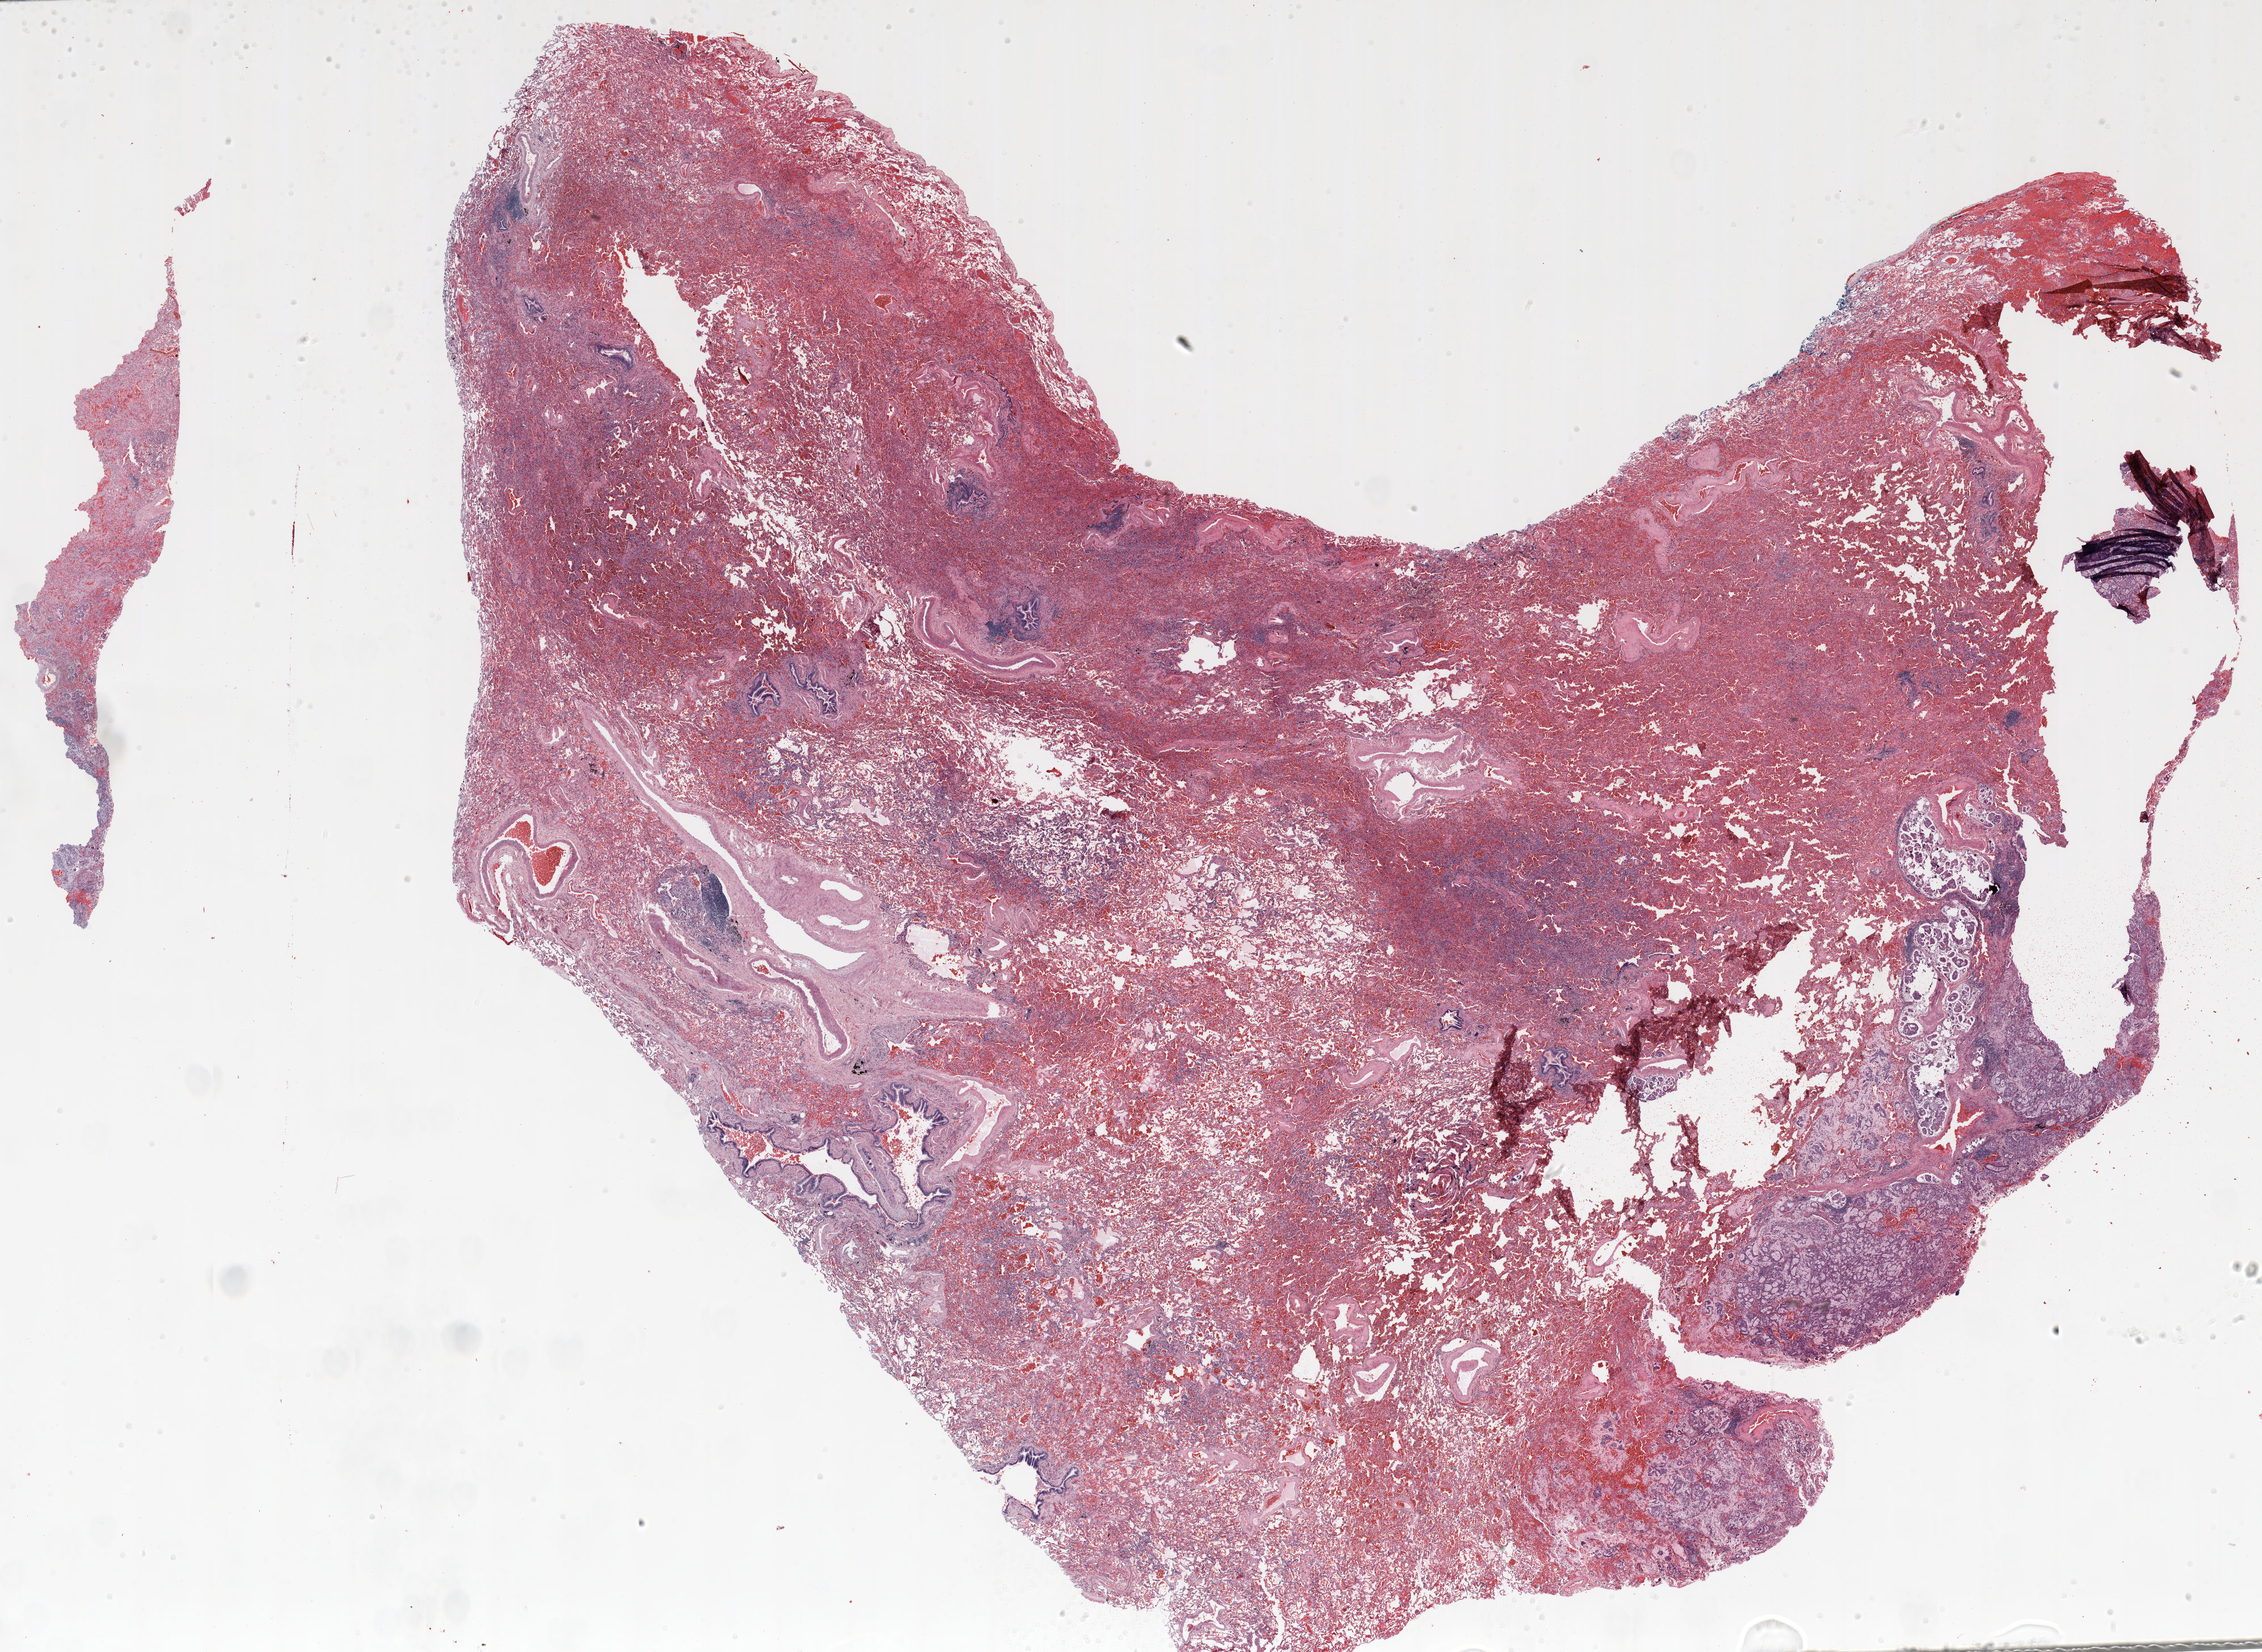
Whole-slide histology image, H&E — shown as a low-resolution overview of the whole scanned area (about 32.0 x 23.4 mm, slide scanned at 20x); formalin-fixed paraffin-embedded (FFPE) section; lung tissue. Male, age 59 at enrolment. Grade: poorly differentiated (G3).
Stage (AJCC 6th edition): IIIA. Participant's lung-cancer diagnosis: Signet ring cell carcinoma. Tumour size (pathology): 21 mm. ICD-O-3 topography: lower lobe of lung (C34.3). Primary tumour location (clinical record): left lower lobe.